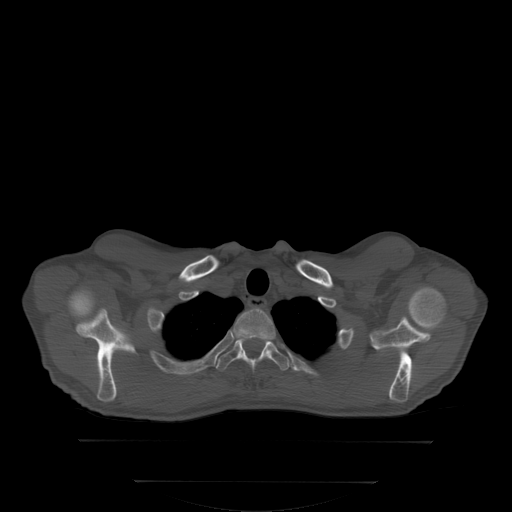
CT including the spine, one axial slice. Slice 282 of 350 in the series (ordered by position). Bone window (W 1800 / L 400 HU). 2.5 mm slice thickness. 512 × 512 image matrix, field of view 500 × 500 mm. Patient: male, 58 years. Case-level facts recorded for this patient, not image findings: primary cancer: prostate; vertebrae with lytic lesions (as recorded): L1.
Annotated regions visible in this slice (semi-automatic segmentation, software-assisted and operator-edited):
- T1 vertebra: box from (x=233, y=308) to (x=276, y=340) px
- T2 vertebra: (x=215, y=338)–(x=290, y=372)